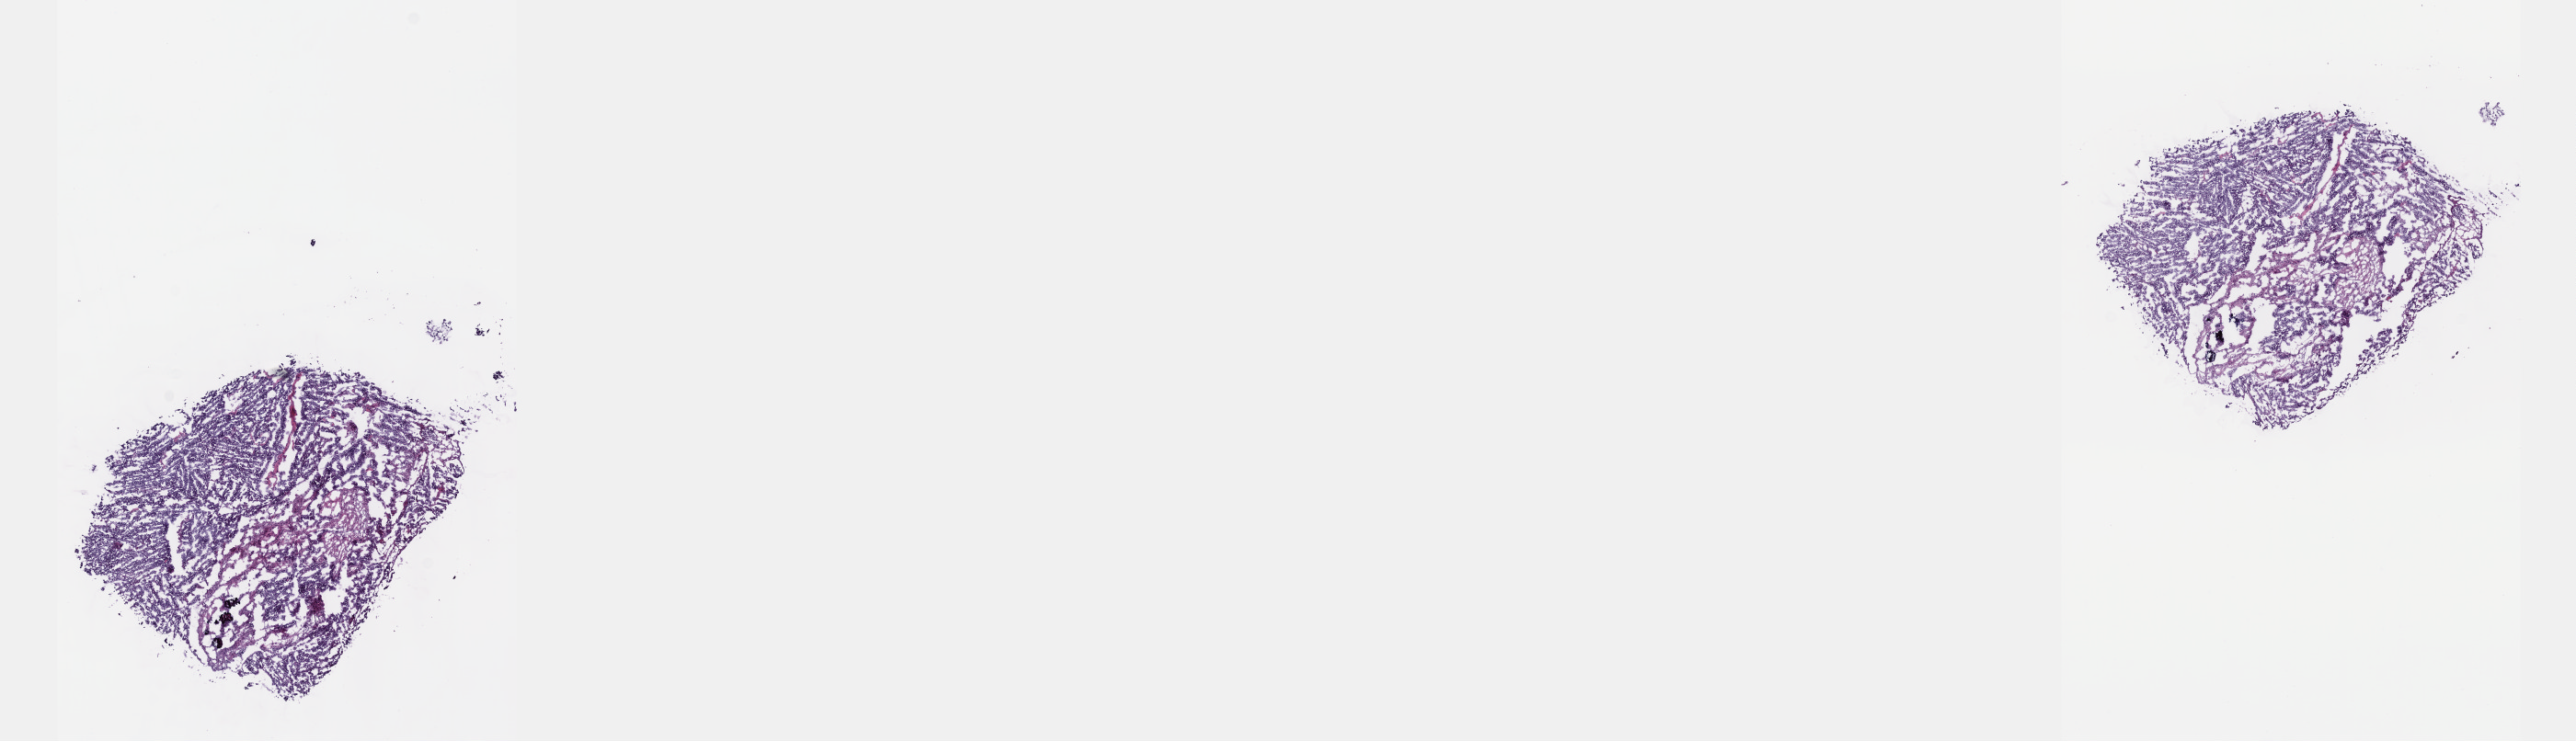
H&E-stained whole-slide image, whole scanned area (about 22.6 x 6.5 mm) shown as a low-resolution overview, formalin-fixed paraffin-embedded (FFPE) diagnostic section, ovary, primary tumour sample. Patient: female, age at initial diagnosis 55 years. Histologic grade: GB (borderline). Pathologist review of this section (percent, as recorded): tumour cells 90%, tumour nuclei 90%, normal cells 0%, stromal cells 10%, necrosis 0%. Infiltration values recorded for this section: lymphocyte infiltration 0%, monocyte infiltration 0%, neutrophil infiltration 0%.
* histologic diagnosis: Papillary serous cystadenocarcinoma
* FIGO stage: IV